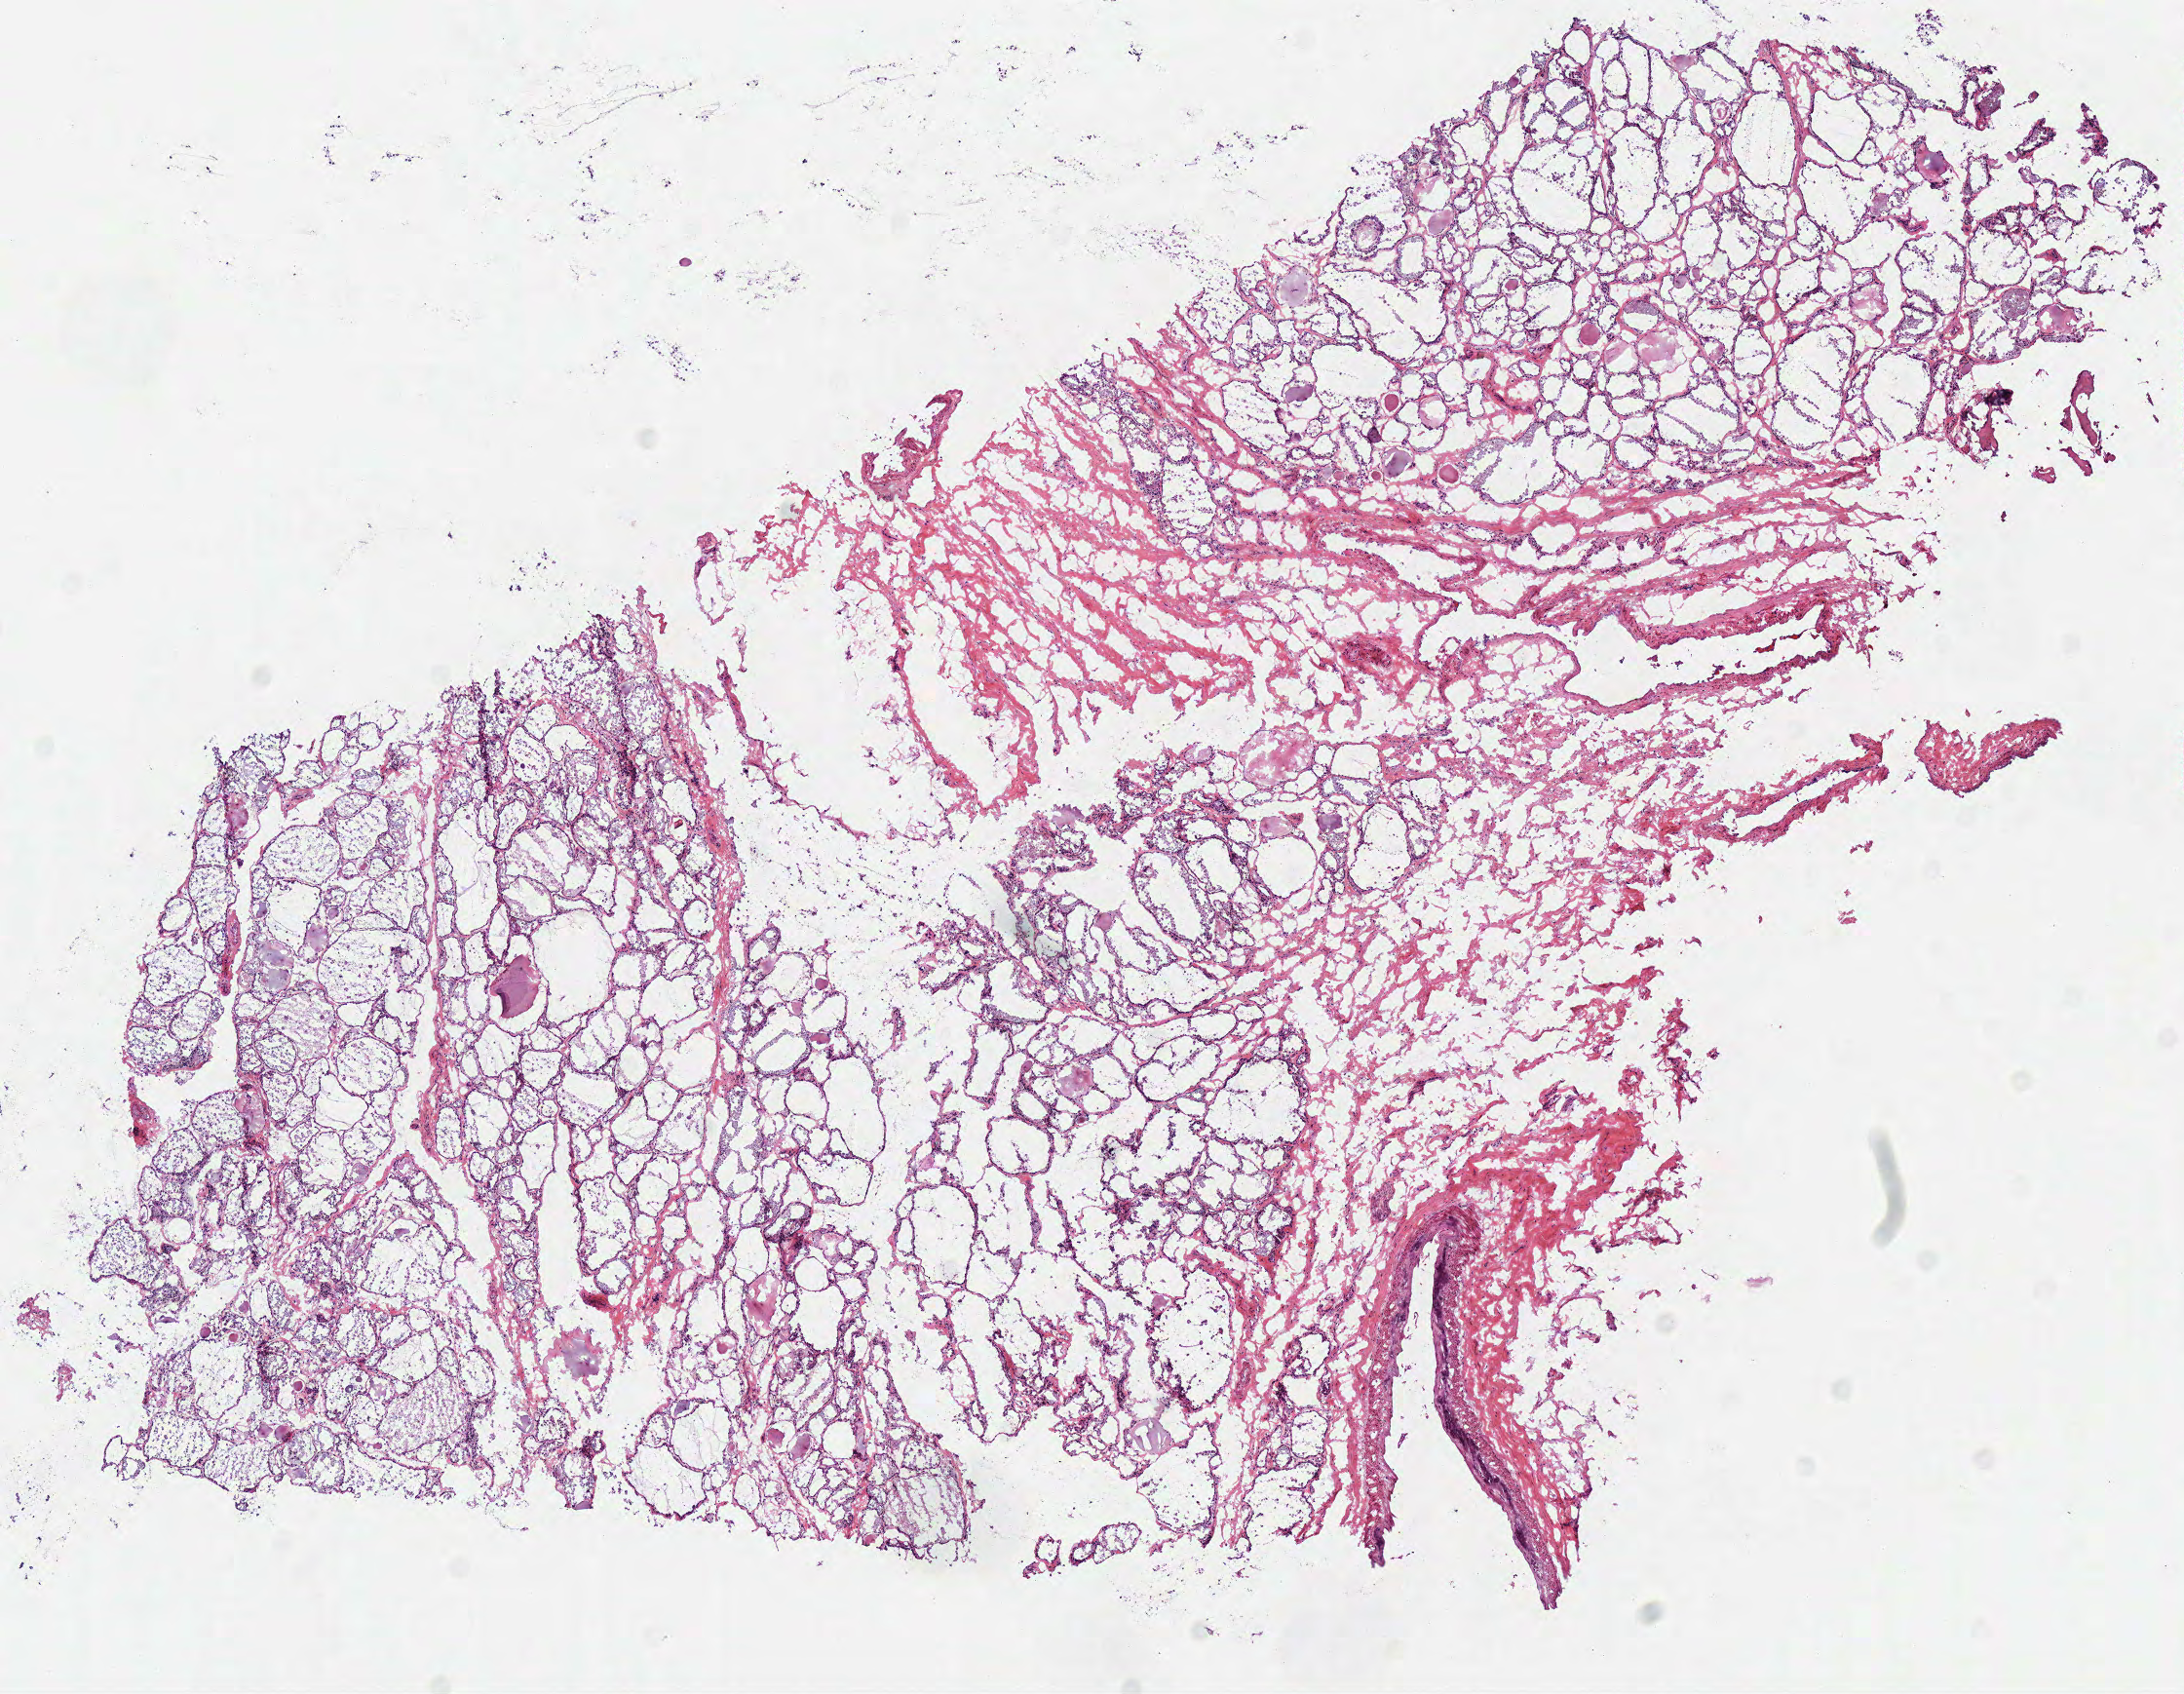
Hematoxylin and eosin (H&E) stained whole-slide image, shown as a low-resolution overview of the whole scanned area (about 8.8 x 6.8 mm); frozen section from the top of the tissue portion; solid tissue normal (non-tumour tissue) sample from the head and neck. Male patient; age at initial diagnosis 74 years.
This section: solid tissue normal (non-tumour) sample from the same patient. Patient diagnosis: Squamous cell carcinoma, NOS (larynx, NOS).